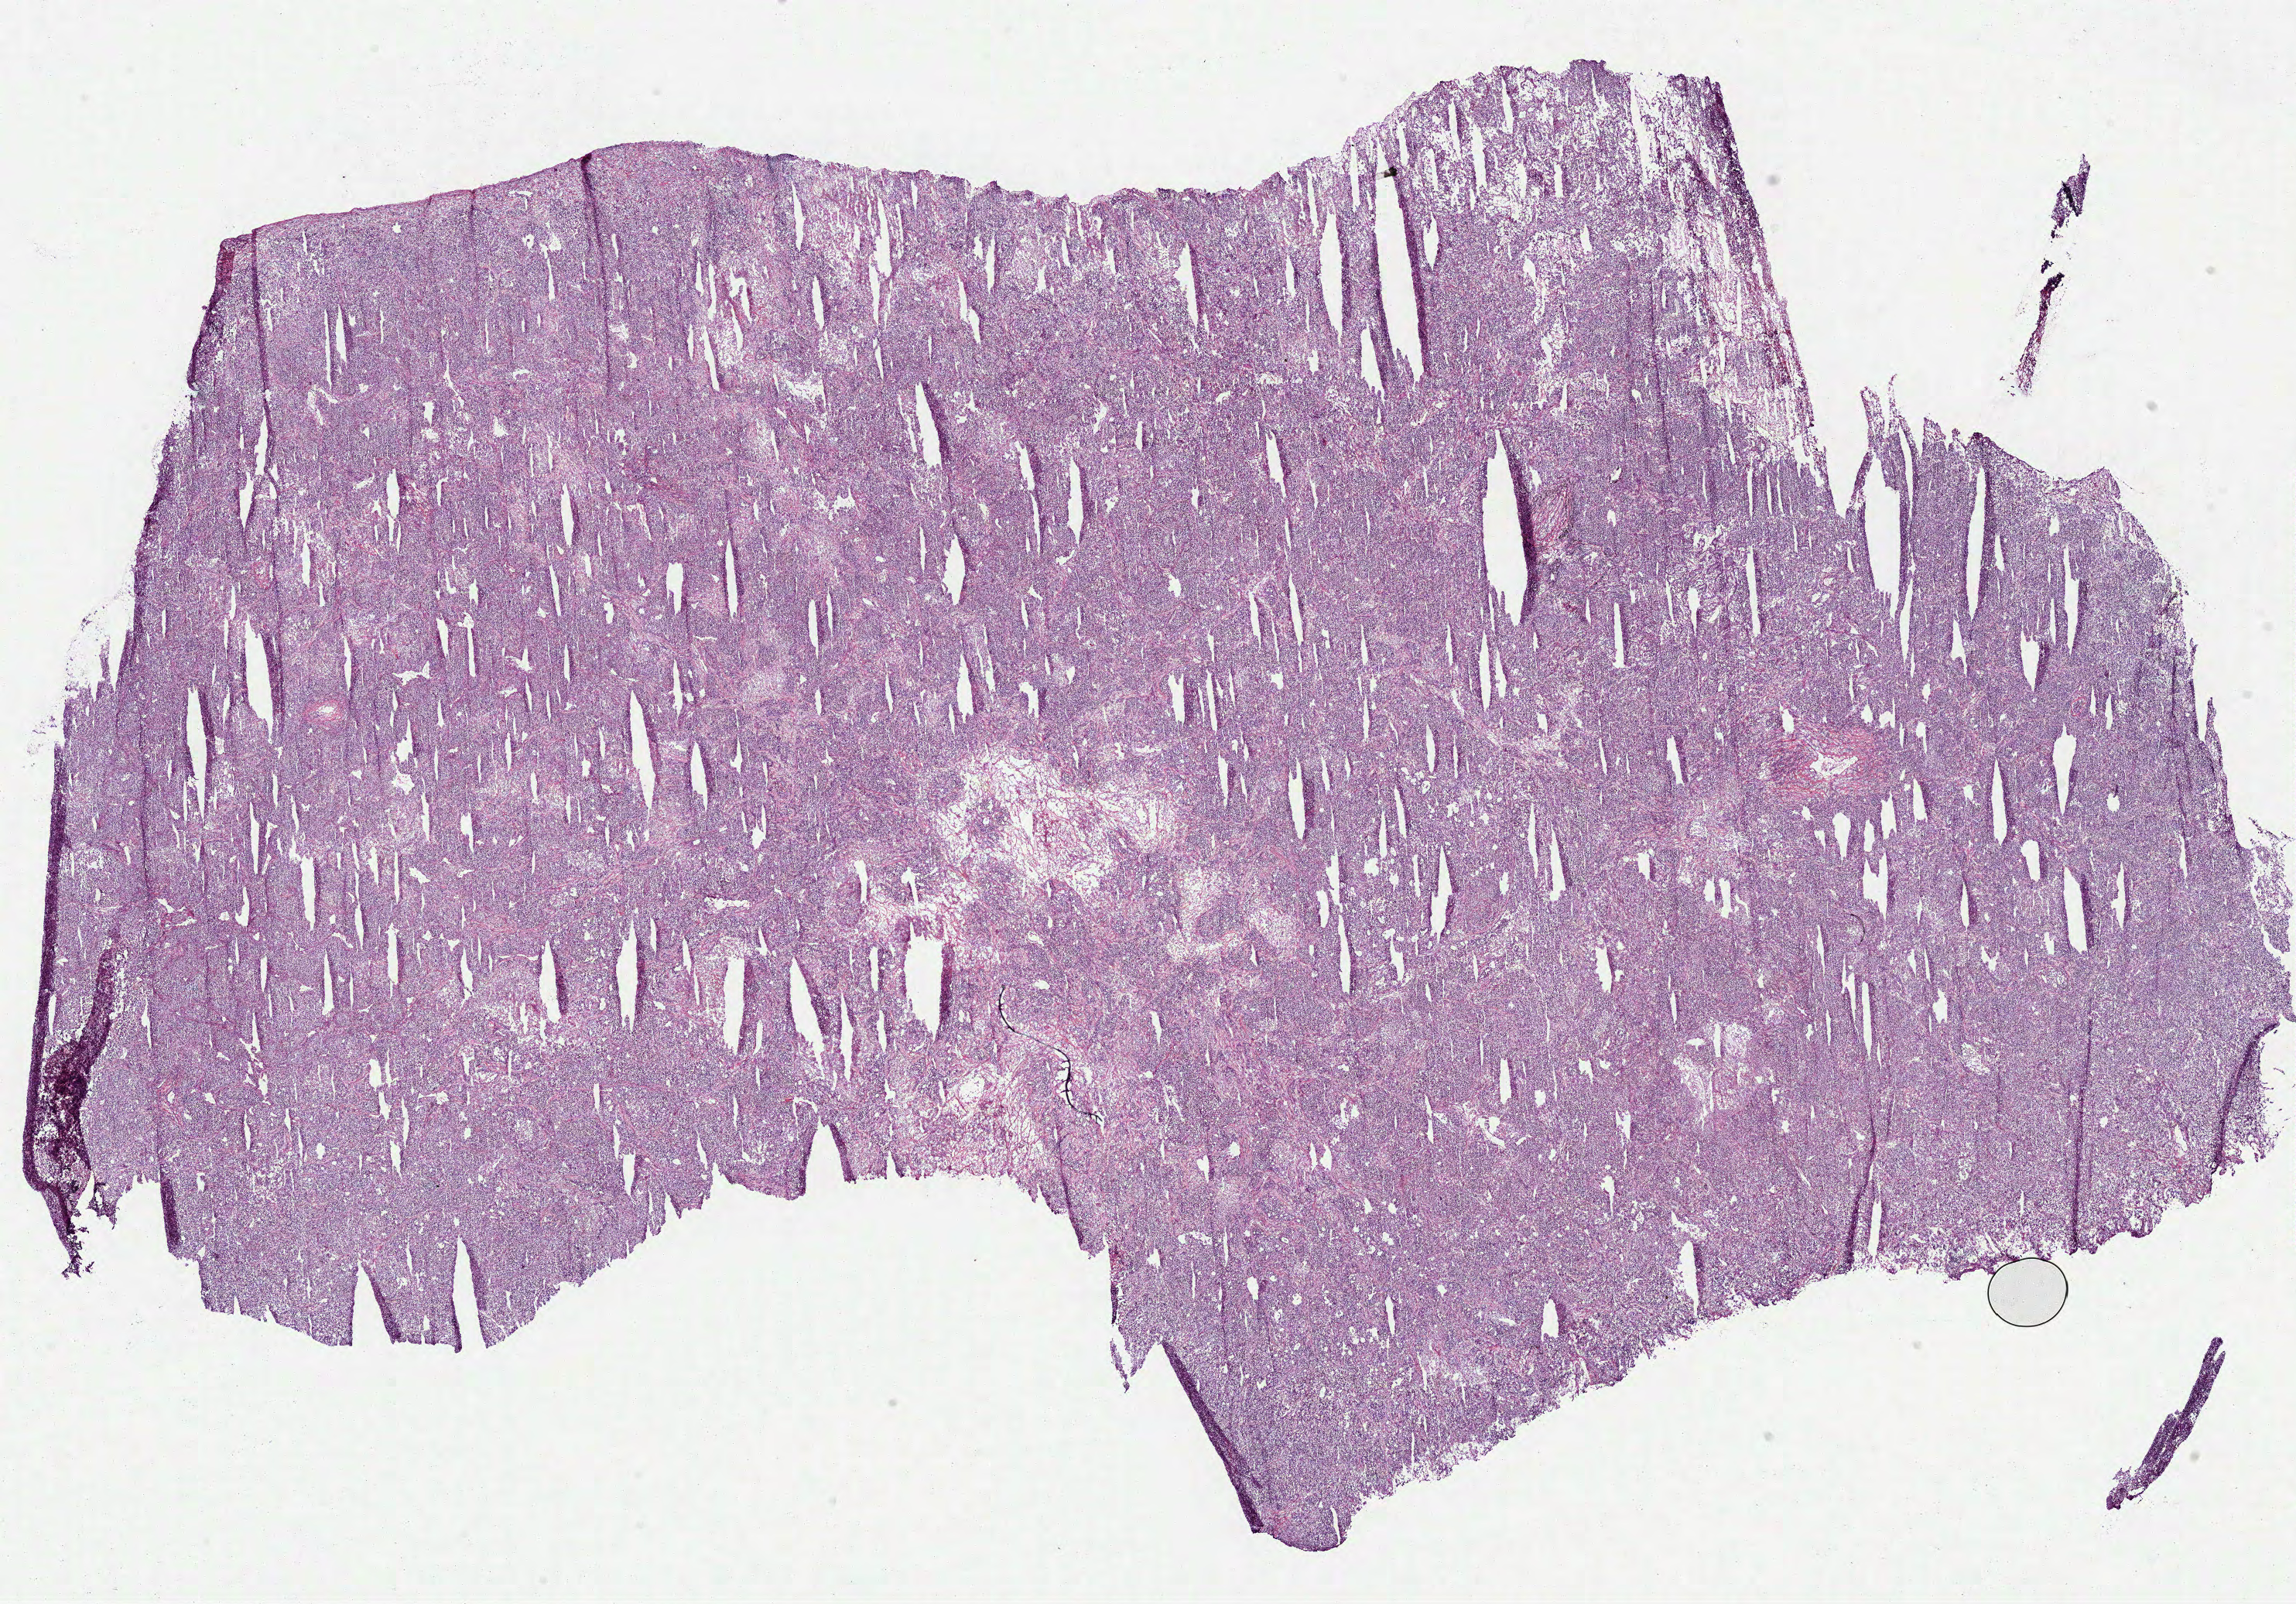
Digitized H&E-stained tissue section (whole slide), whole scanned area (about 23.9 x 16.7 mm) shown as a low-resolution overview, frozen section from the top of the tissue portion, primary tumour sample from the lung. Female, age 69 years at initial diagnosis. Composition of this section per pathologist review: tumour cells 78%, tumour nuclei 80%, normal cells 0%, stromal cells 10%, necrosis 12%.
• diagnosis: Bronchiolo-alveolar adenocarcinoma, NOS (upper lobe, lung)
• AJCC pathologic stage: IA
• TNM: T1b N0 M0
• laterality: left